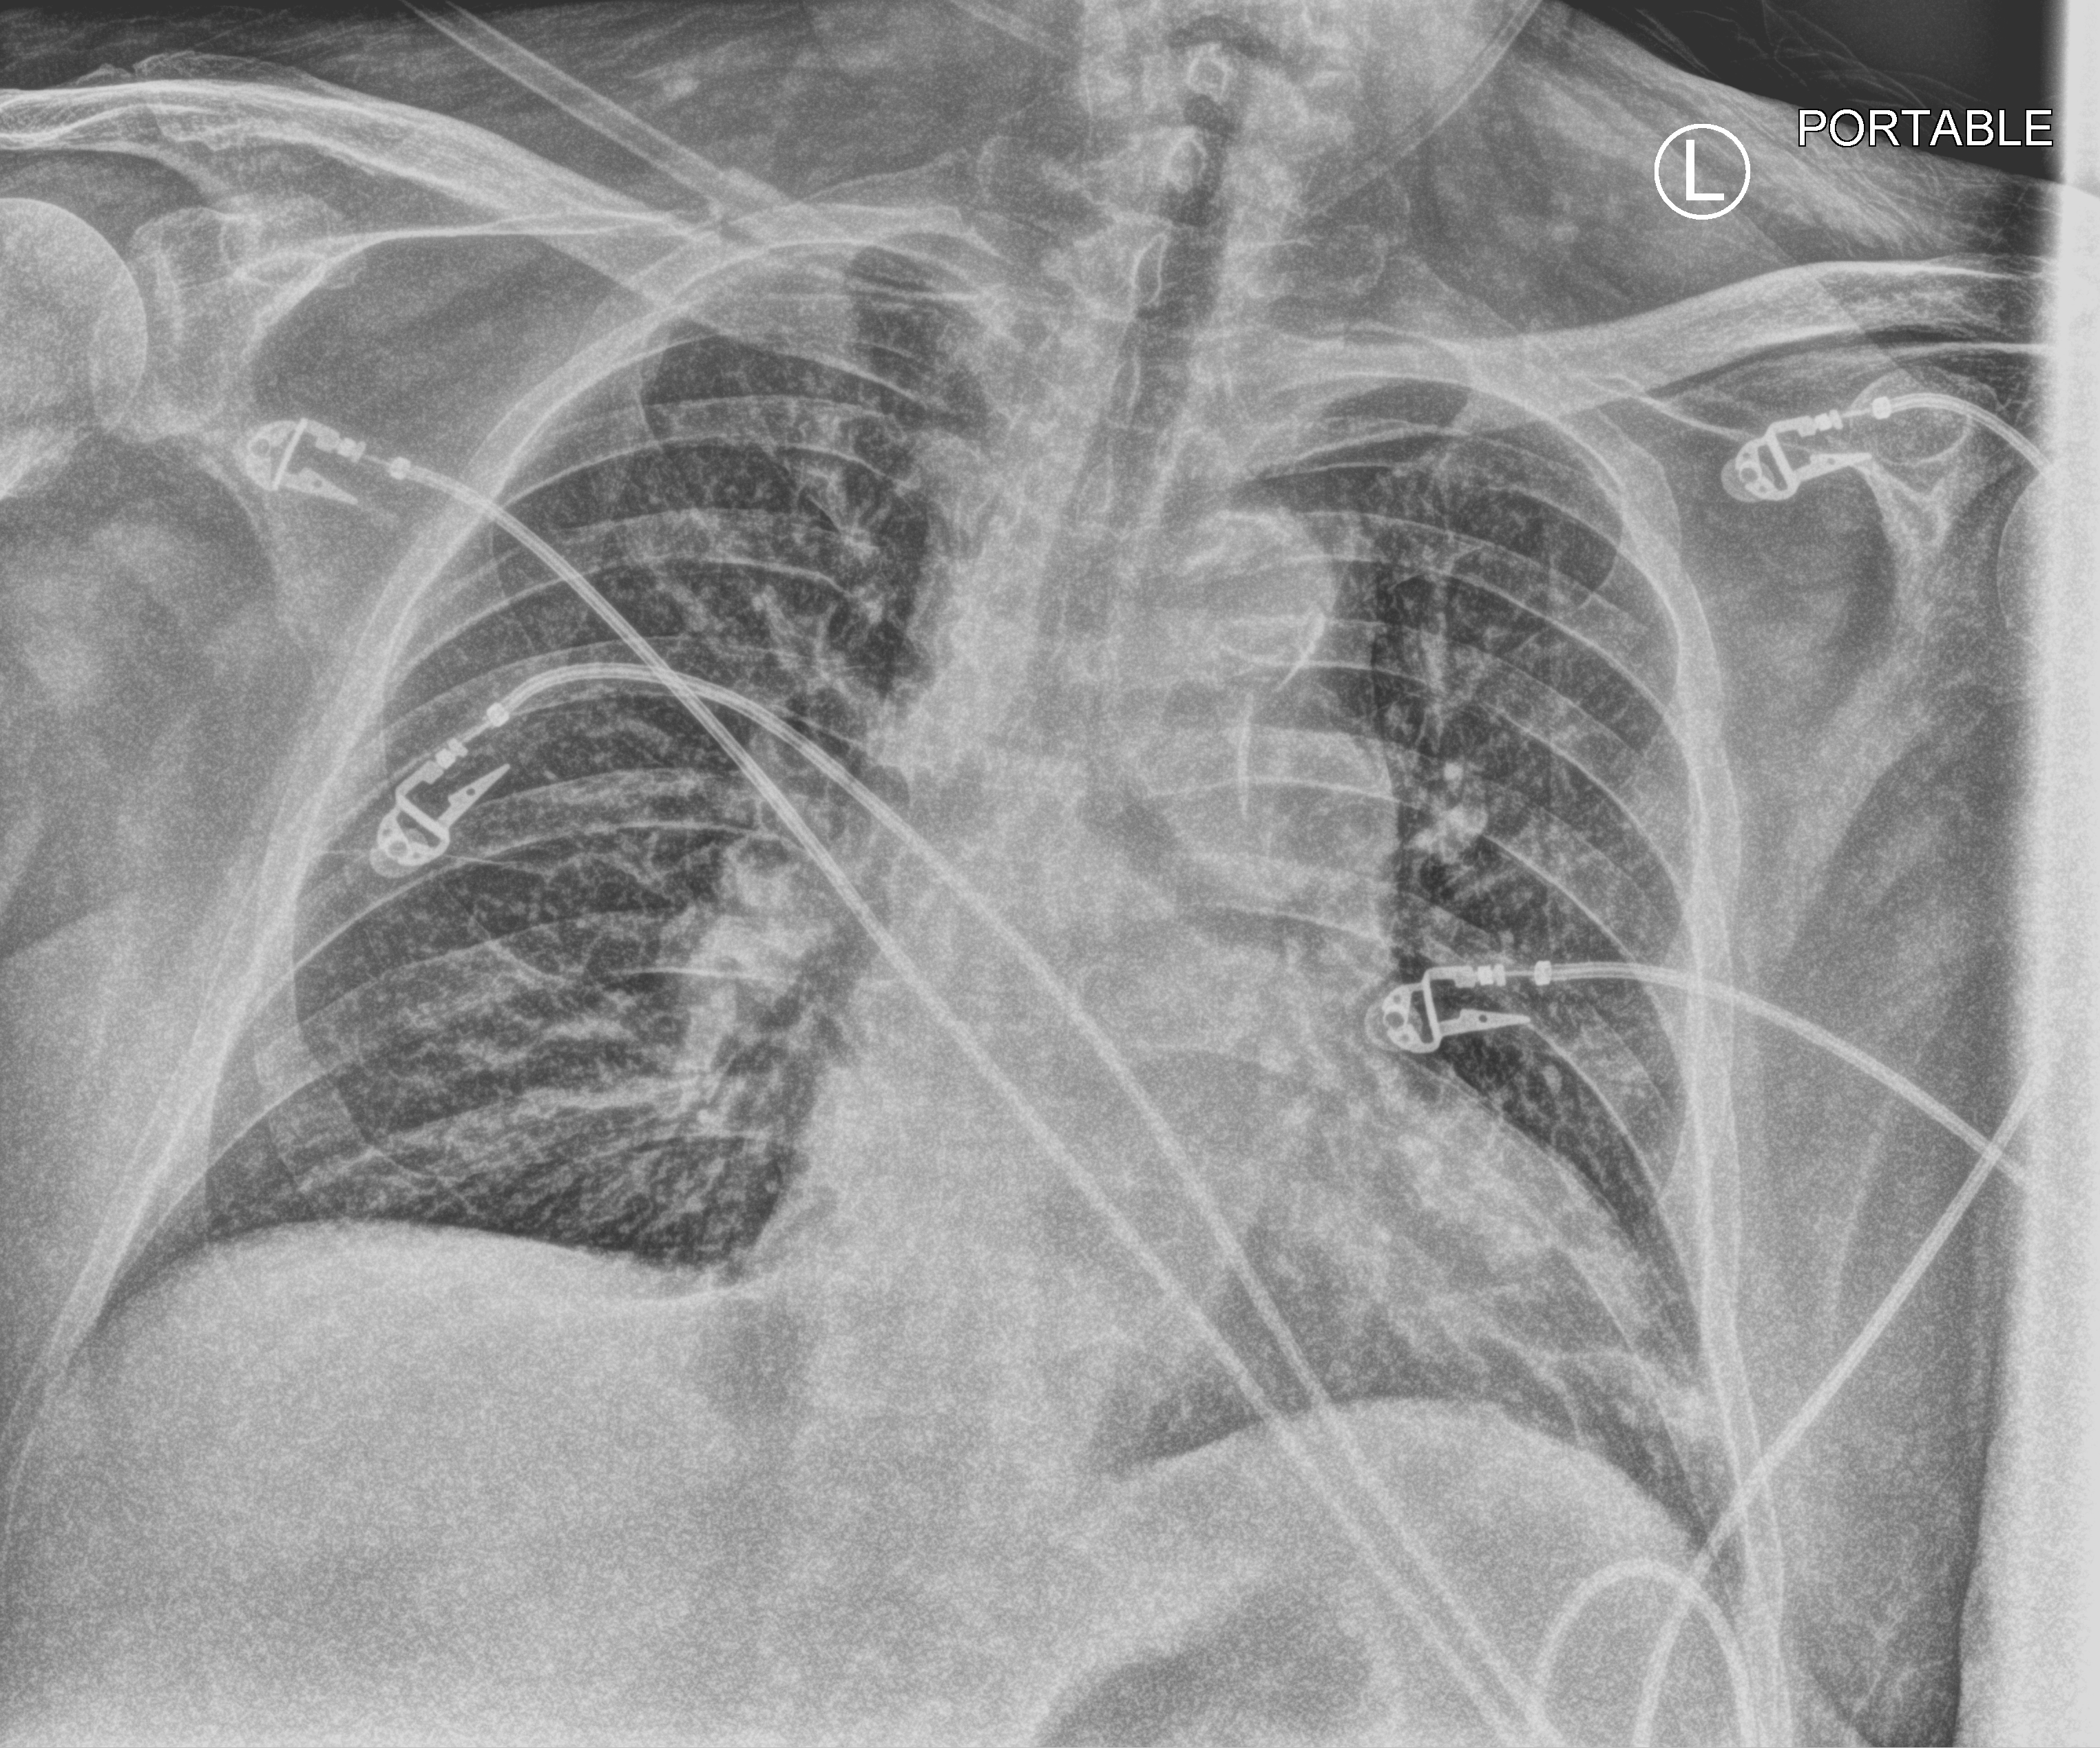
Bedside chest radiograph (computed radiography). Patient hospitalised with COVID-19; male, aged 75–90 years.
From the hospital-stay record, not from the radiograph (when in the stay this image was taken is not recorded):
- admitted to intensive care during this hospital stay: no
- mechanically ventilated during this hospital stay: no